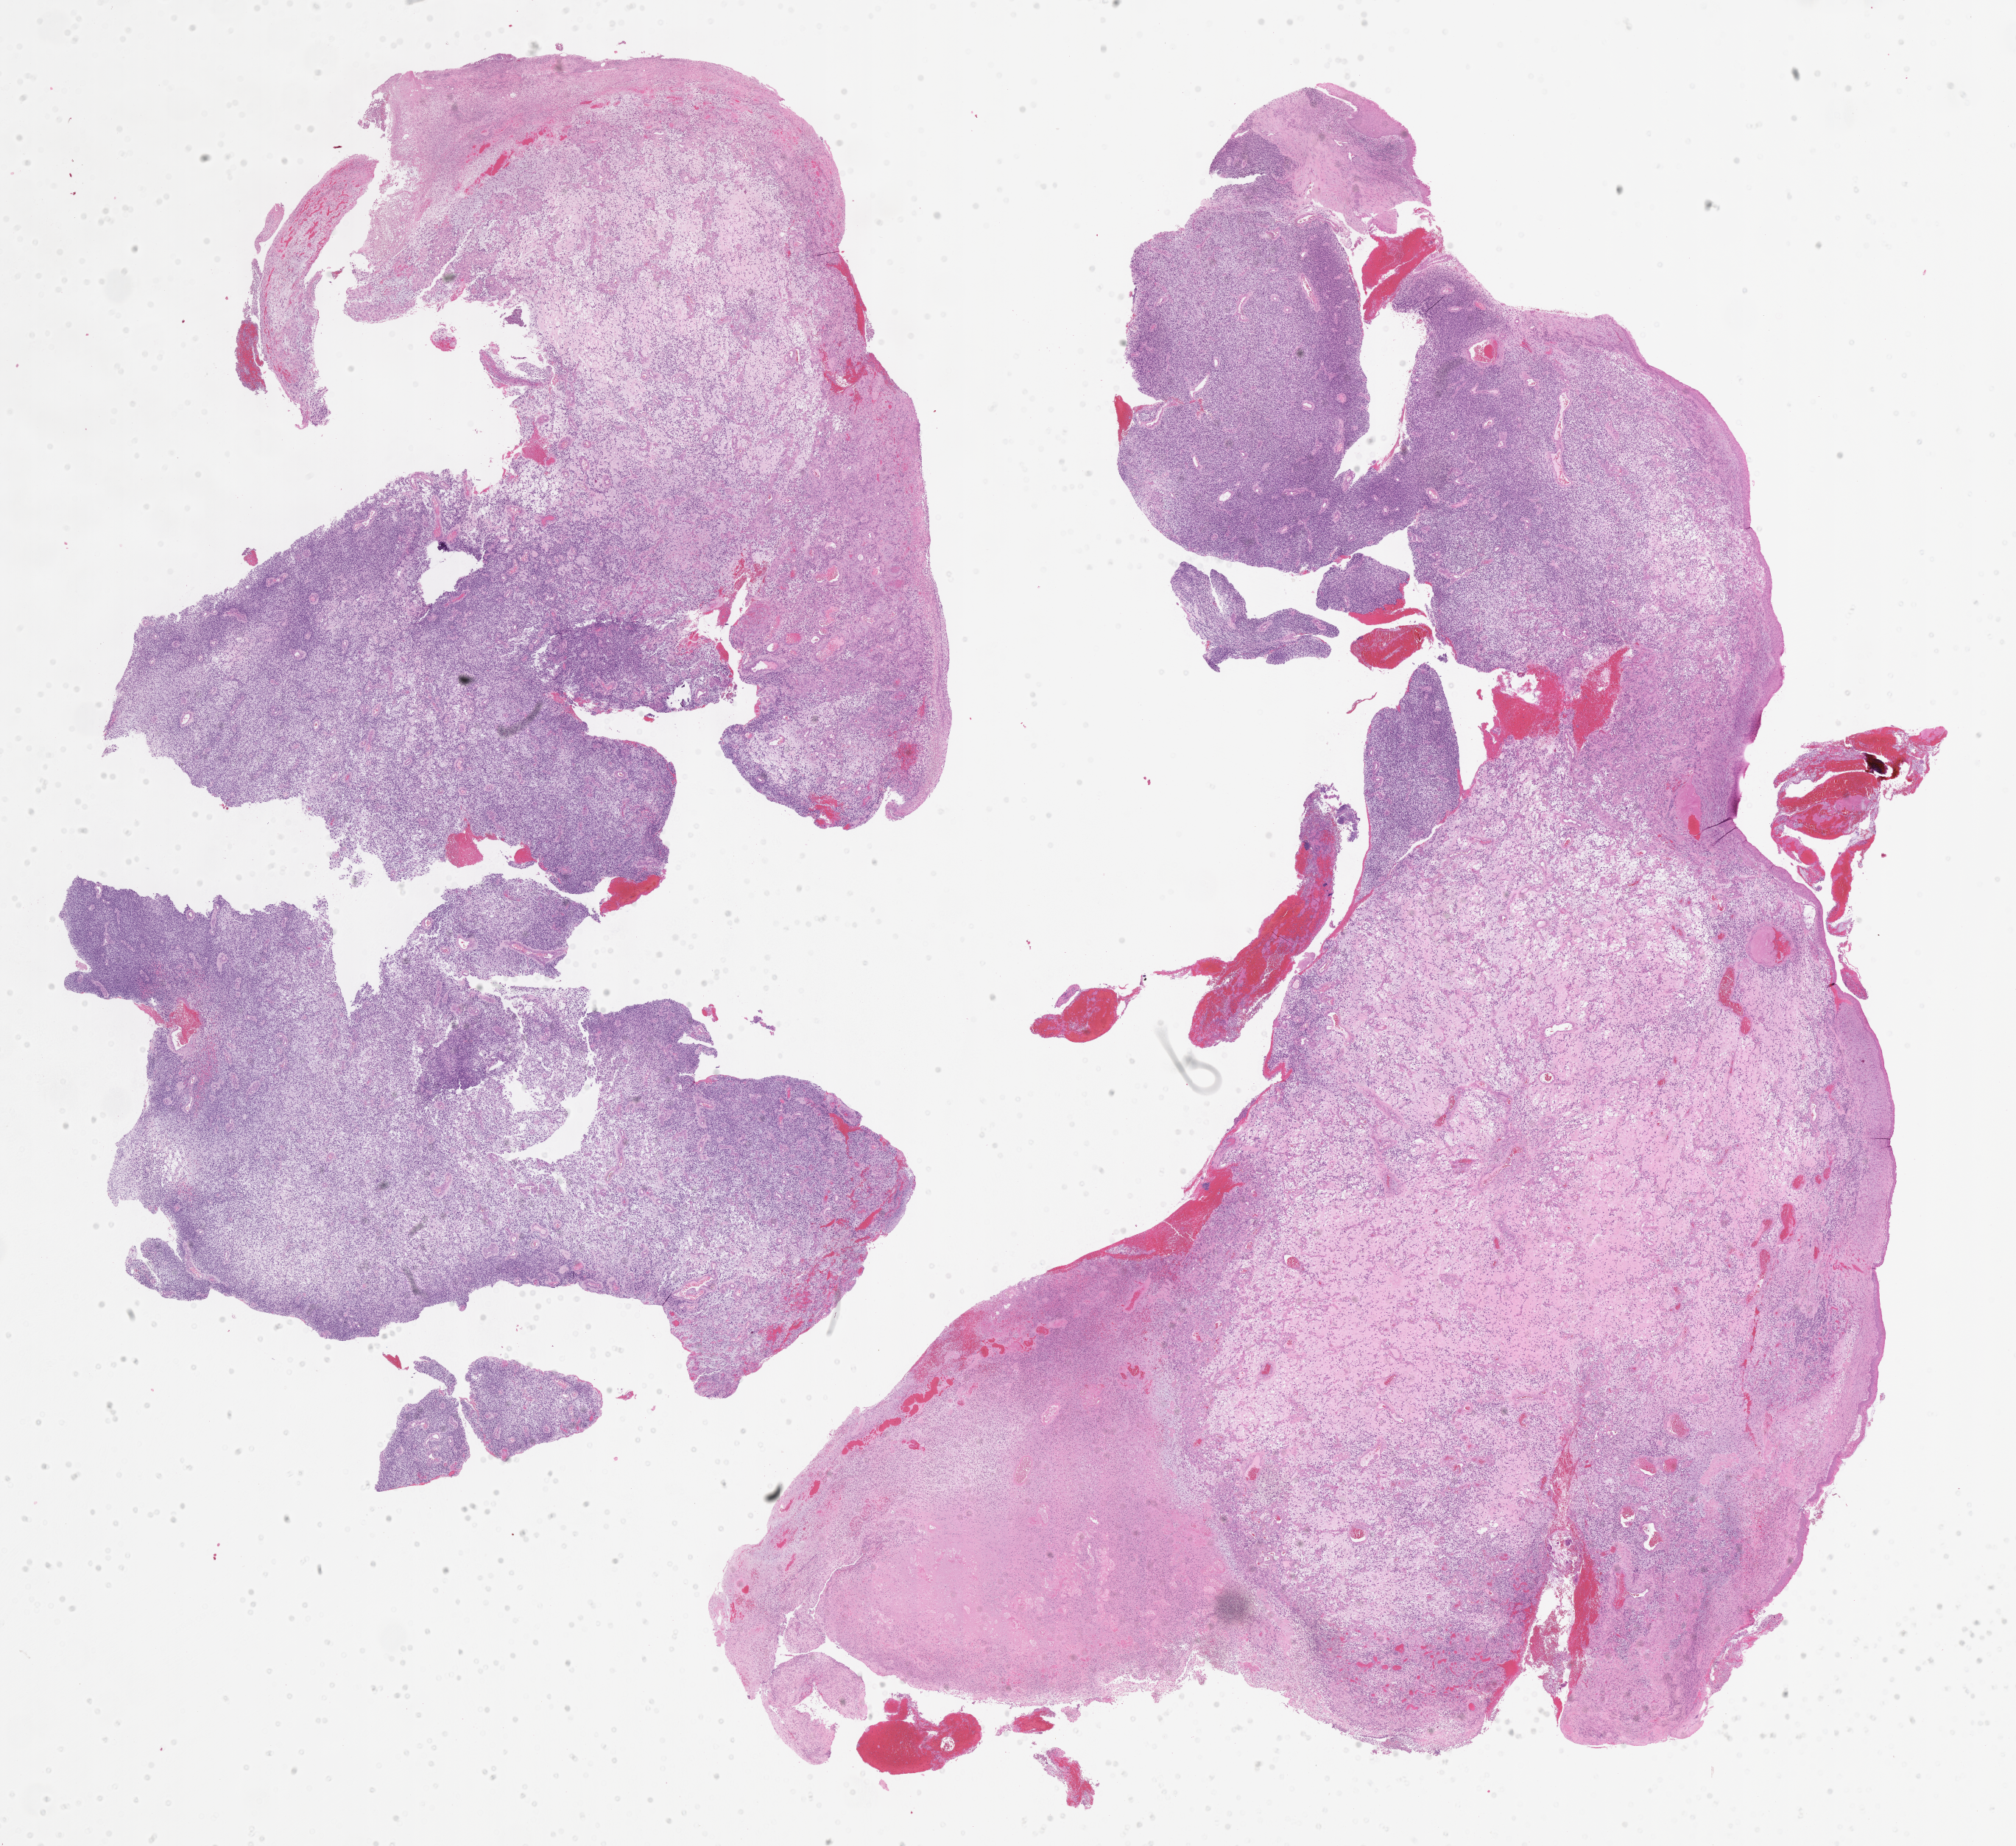
Haematoxylin and eosin whole-slide image of tumor tissue — whole scanned area (about 22.1 x 20.3 mm) shown as a low-resolution overview, formalin-fixed, paraffin-embedded (FFPE) tissue, sample anatomic site: nasopharynx. Patient: male, age 7.1 years at diagnosis.
Diagnosis: rhabdomyosarcoma; histological classification: embryonal rhabdomyosarcoma. Metastatic status at presentation (as recorded): non-metastatic (unconfirmed). Stage (as recorded): 3.